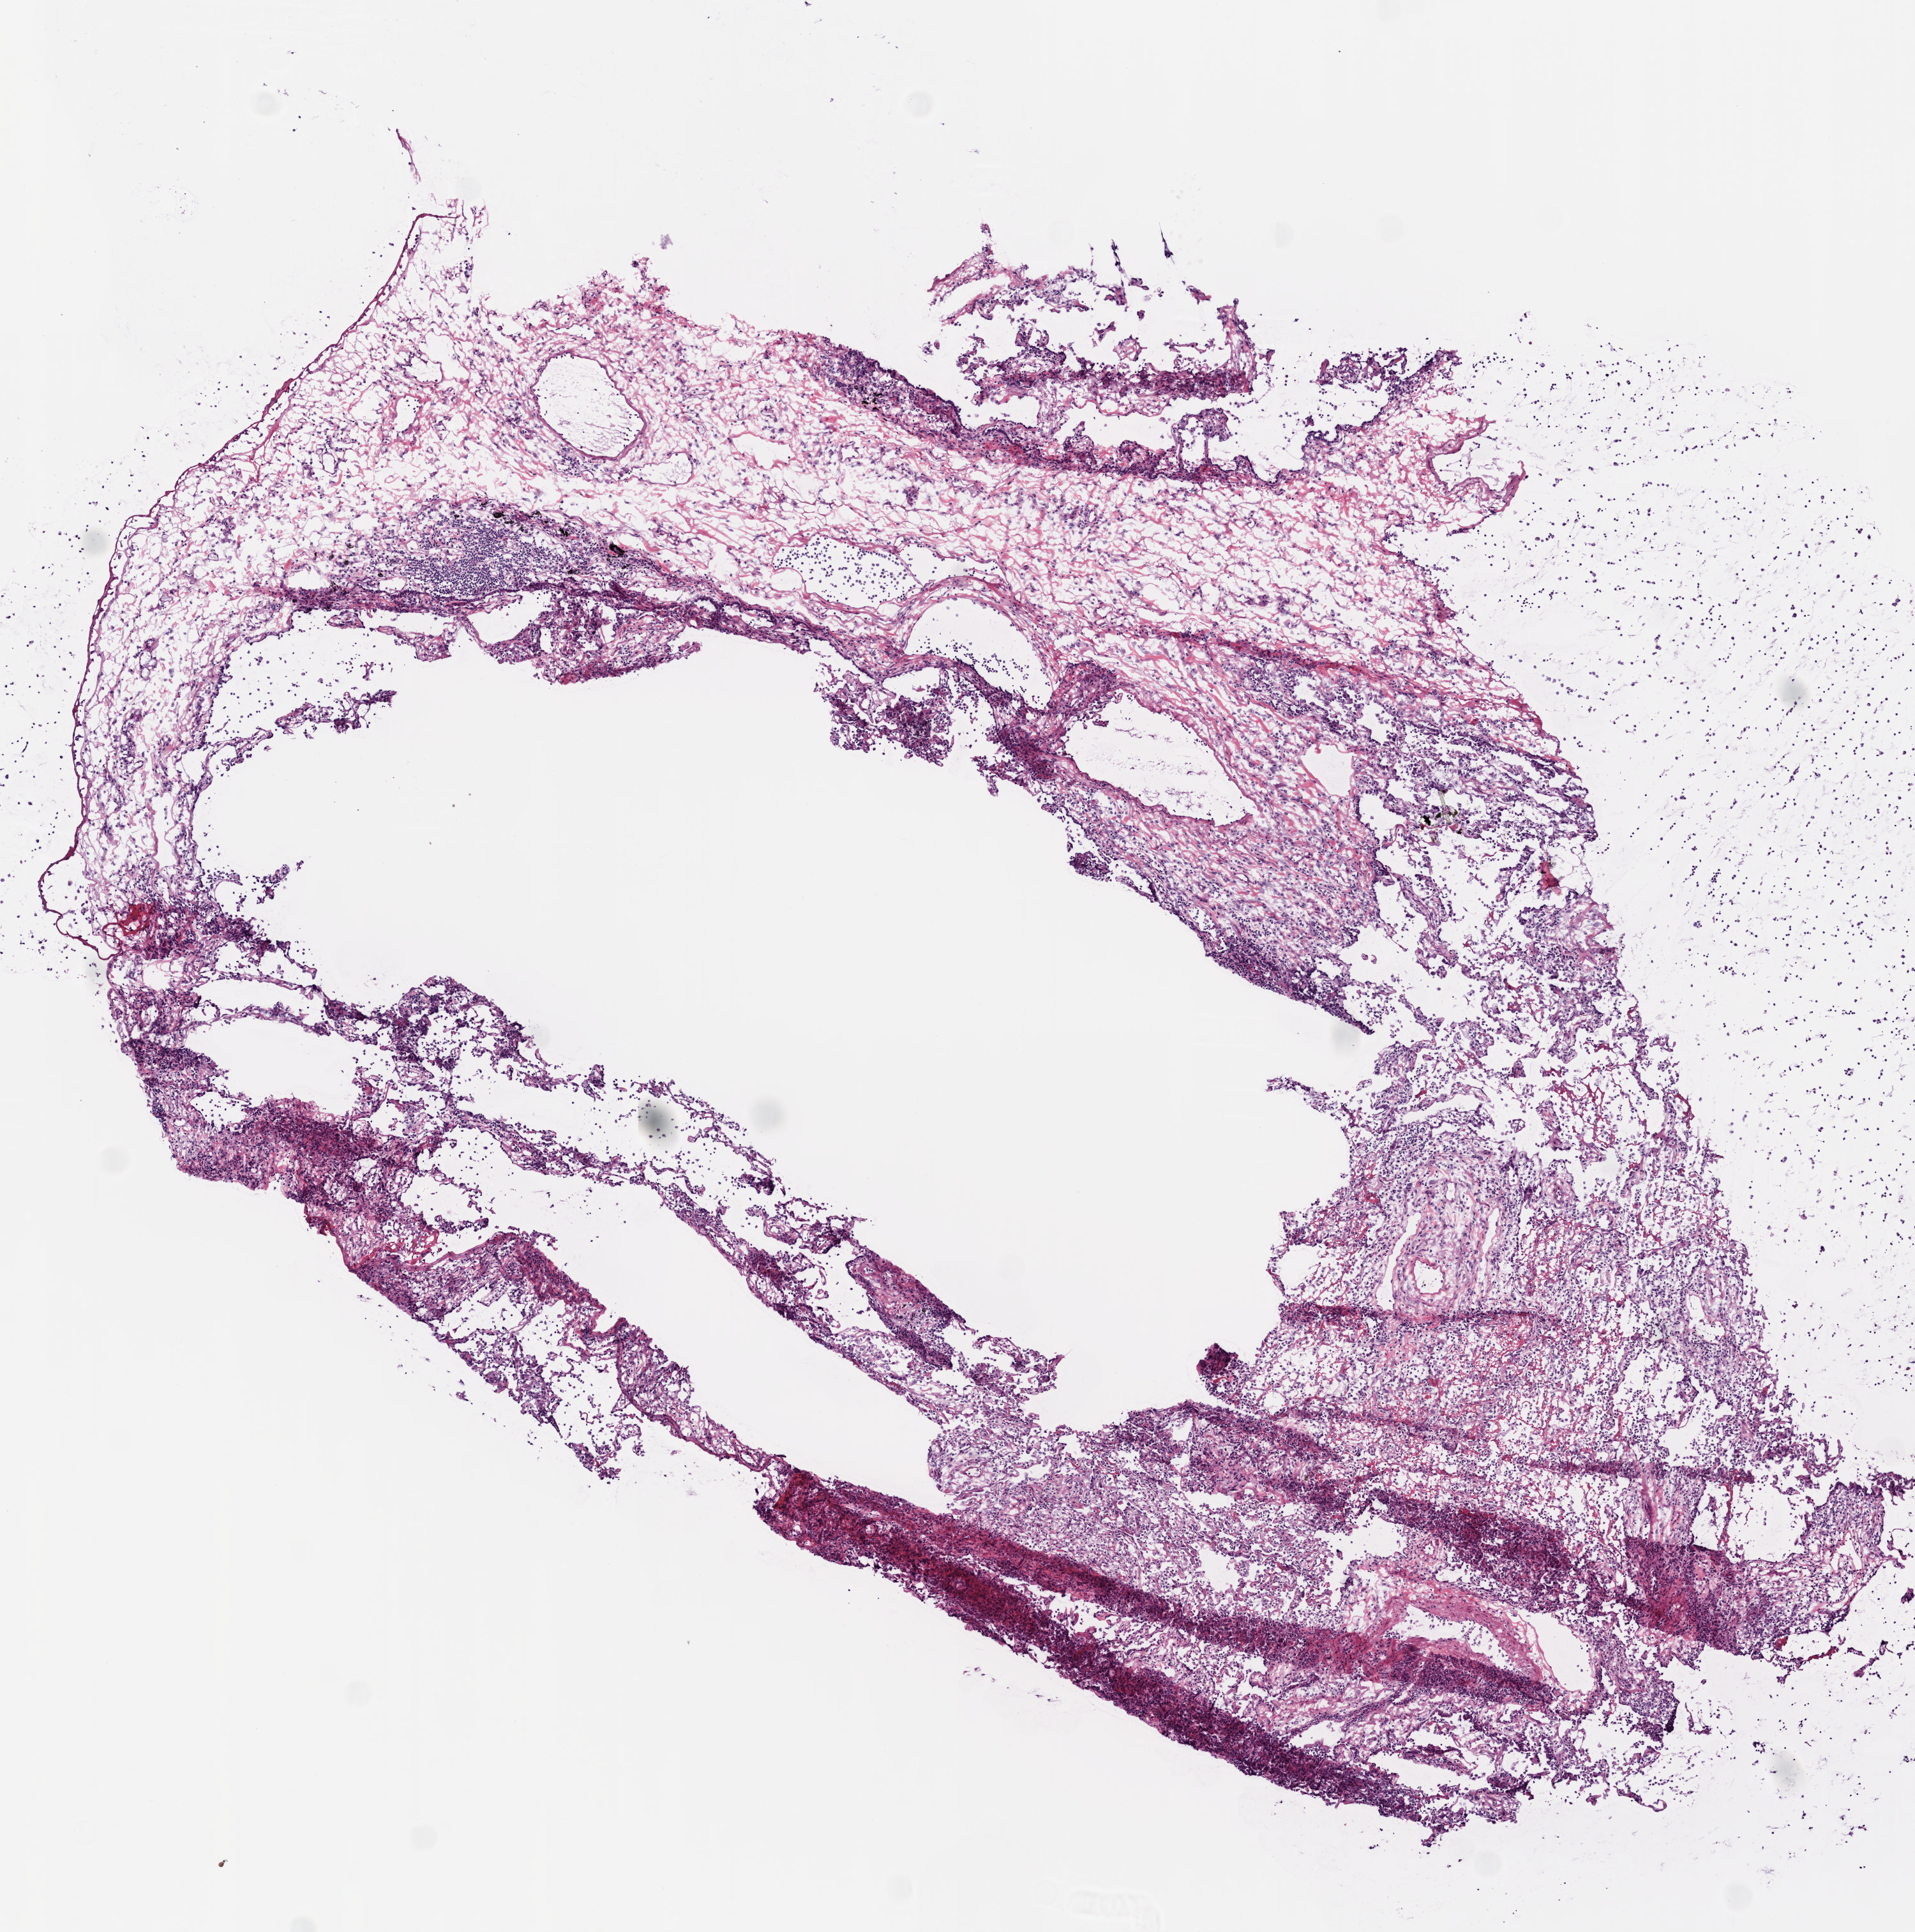
Whole-slide histology image, Hematoxylin and eosin (H&E) stained — shown as a low-resolution overview of the whole scanned area (about 6.0 x 6.1 mm), frozen section from the top of the tissue portion, lung, solid tissue normal (non-tumour tissue) sample. Male patient; age at initial diagnosis 71 years.
This section: solid tissue normal (non-tumour) sample from the same patient. Patient diagnosis: Squamous cell carcinoma, NOS (upper lobe, lung).